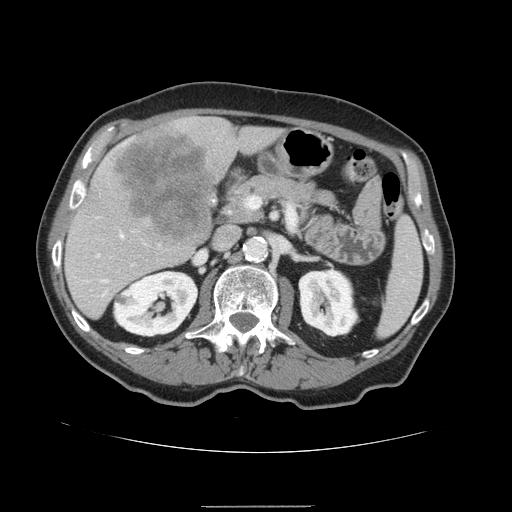
Contrast-enhanced abdominal CT, one axial slice. Position 75 of 168 along the scan axis. 120 kVp. Intravenous contrast given. Soft-tissue window (W 400 / L 40 HU). 2.5 mm slice thickness. 512 × 512 image matrix, field of view 386 × 386 mm. Male patient, age 74 years. From the clinical record (not read from this slice): diagnosis: colorectal cancer liver metastases, imaged before liver resection; multiple liver metastases: no; largest metastasis: 14.5 cm; disease in both lobes: yes.
Annotated regions visible in this slice (manually delineated by an expert):
- hepatic veins: bounding box <121,235,123,237> (left, top, right, bottom; pixels)
- liver: <65,116,285,319>
- planned liver remnant (the part of the liver to remain after resection): <65,126,284,319>
- liver metastasis: <112,126,217,243>